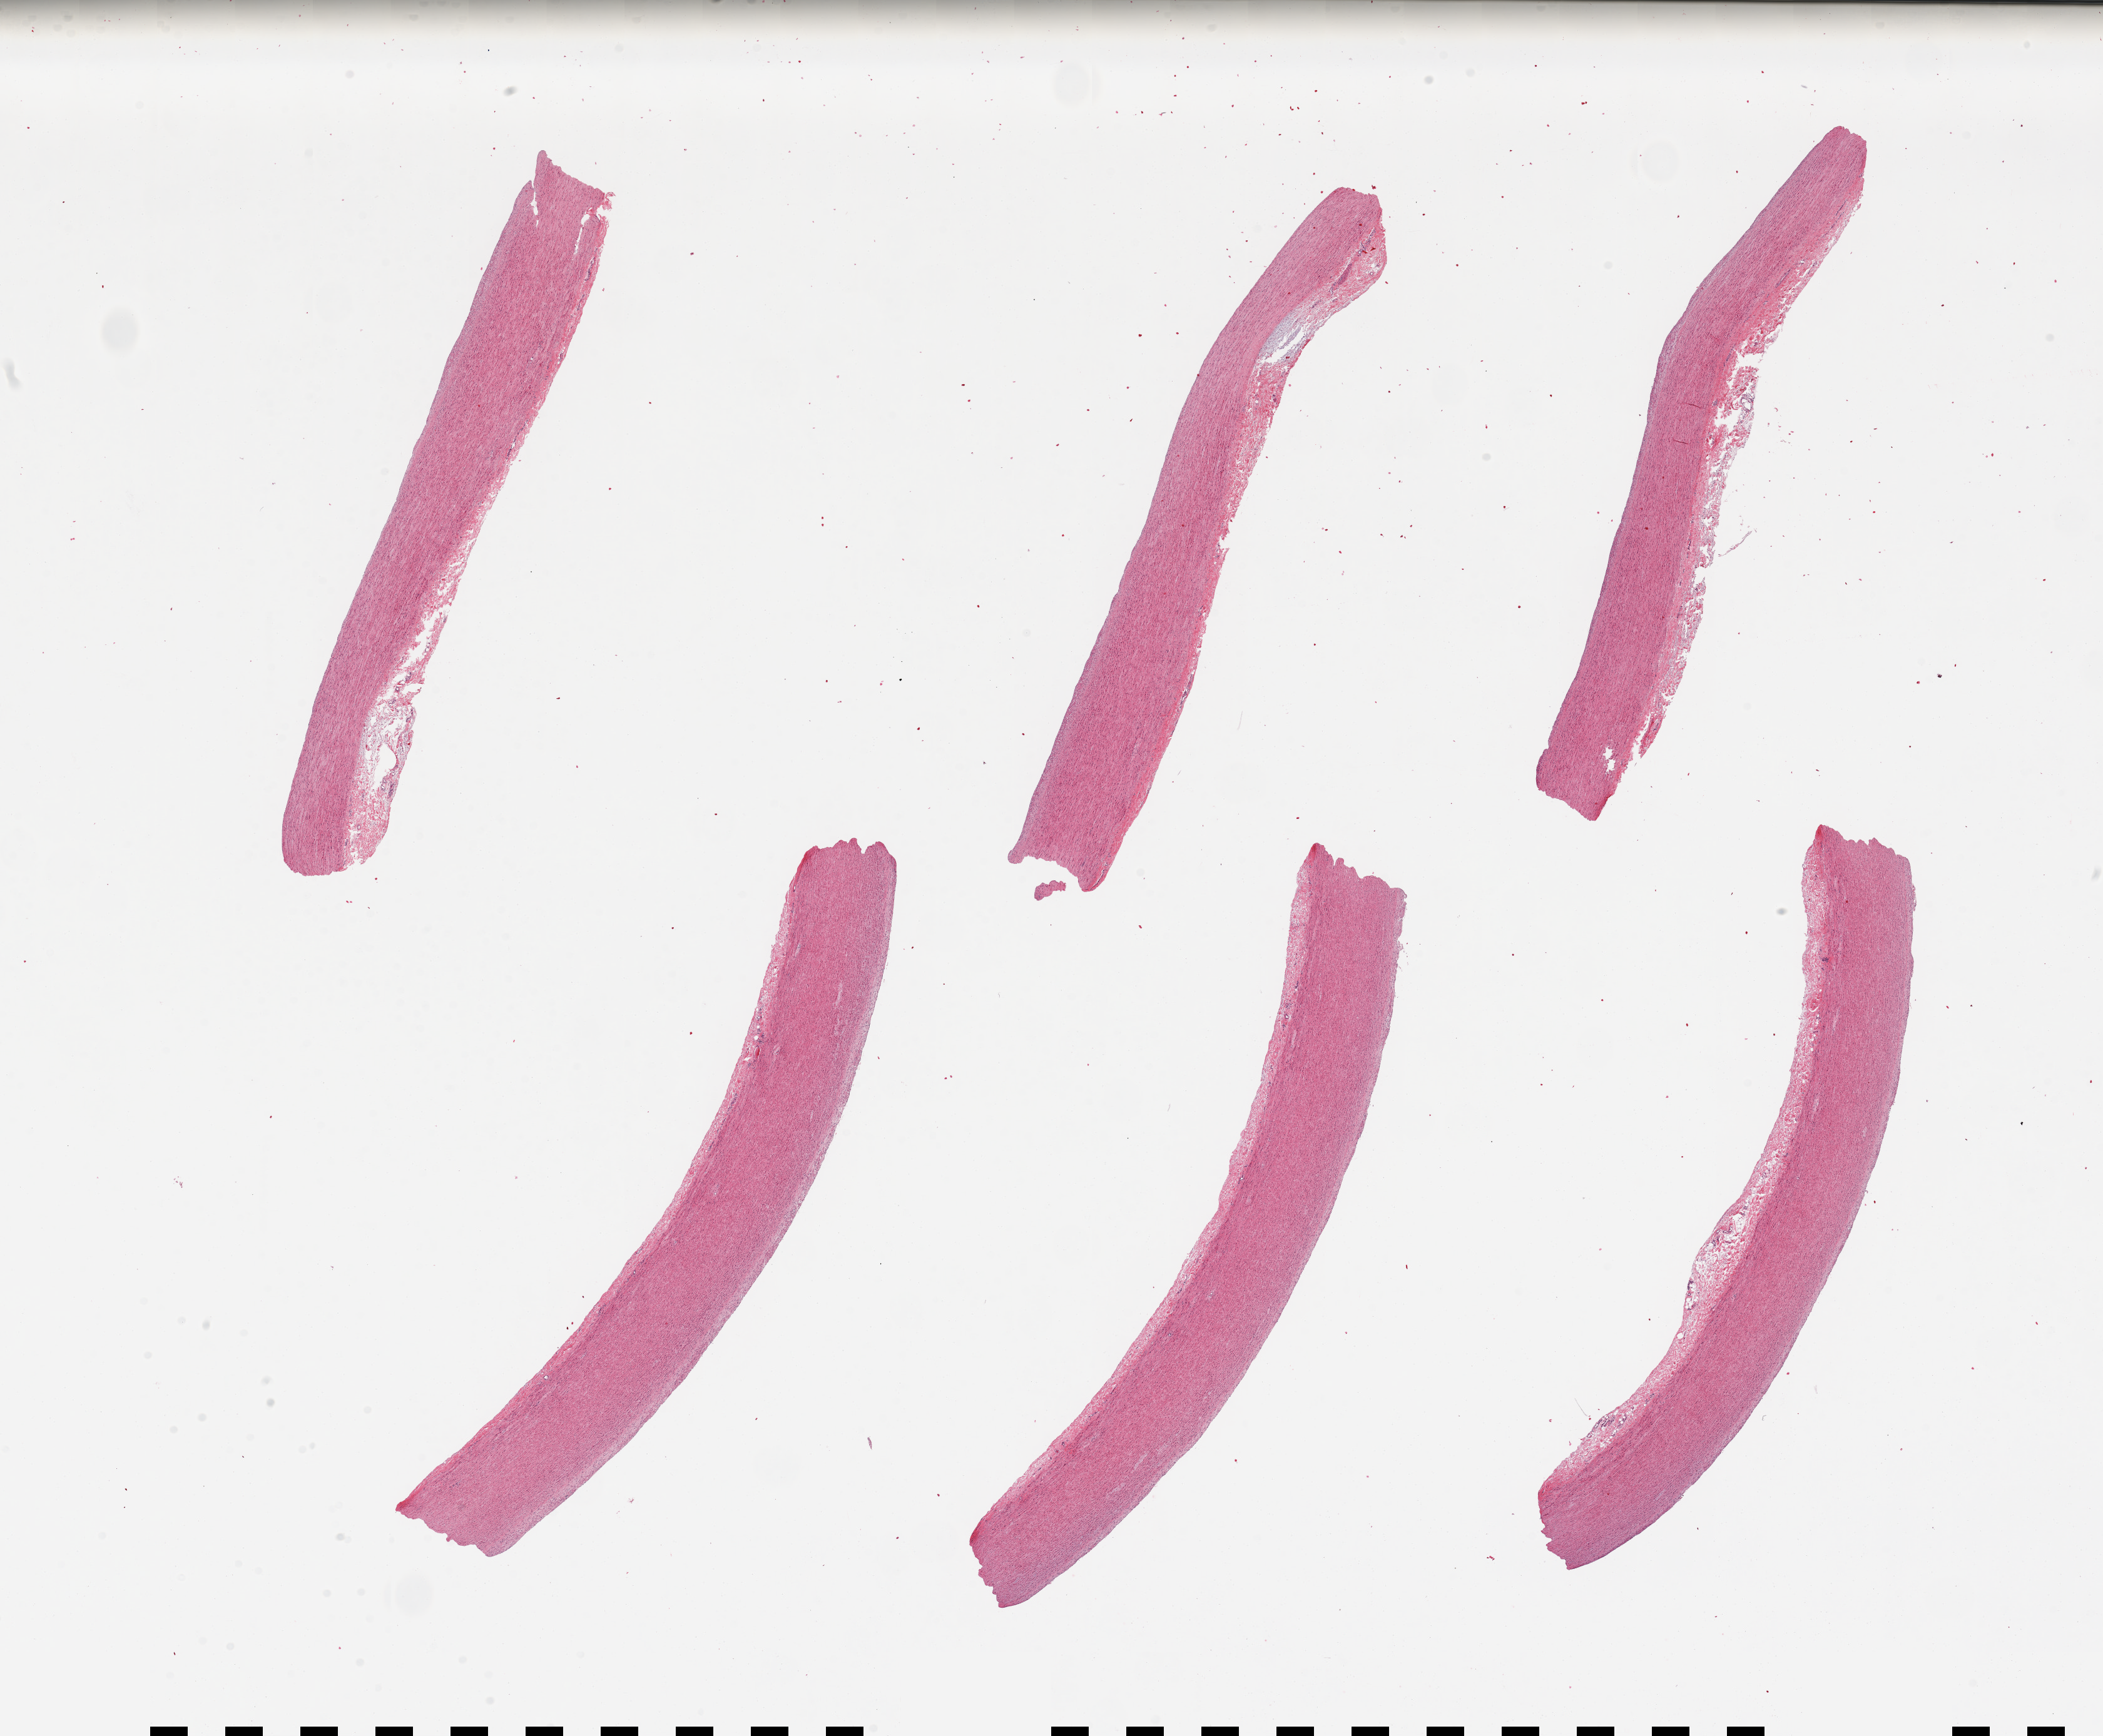
Haematoxylin and eosin whole-slide image, brightfield — low-resolution overview of the scanned area, about 26.6 x 21.9 mm, PAXgene-fixed, paraffin-embedded tissue, sampled site (target tissue): aorta, donor tissue sample. Donor sex: male.
* review note (as recorded): 6 pieces, up to ~0.5mm adherent serosa on most